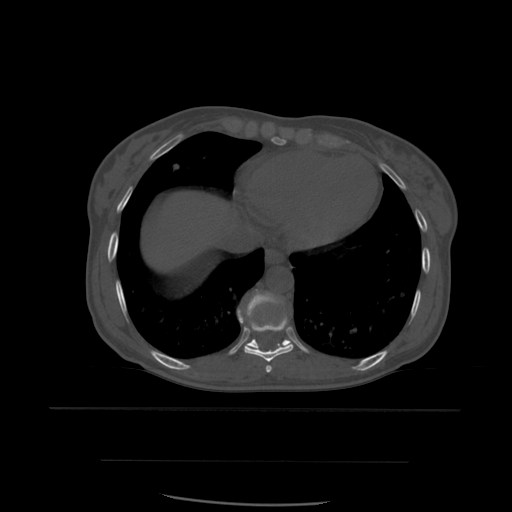
CT including the spine, one axial slice. Slice 330 of 574 in the series (ordered by position). Bone window (W 1800 / L 400 HU). 512 × 512 image matrix, field of view 392 × 392 mm. Patient age 48 years. Case-level facts recorded for this patient, not image findings: primary cancer: lung.
Annotated regions visible in this slice (semi-automatically segmented with operator editing):
- T10 vertebra: bounding box (x1, y1, x2, y2) in pixels: (238, 290, 290, 348)
- T8 vertebra: (266, 366, 273, 373)
- T9 vertebra: (239, 311, 294, 362)